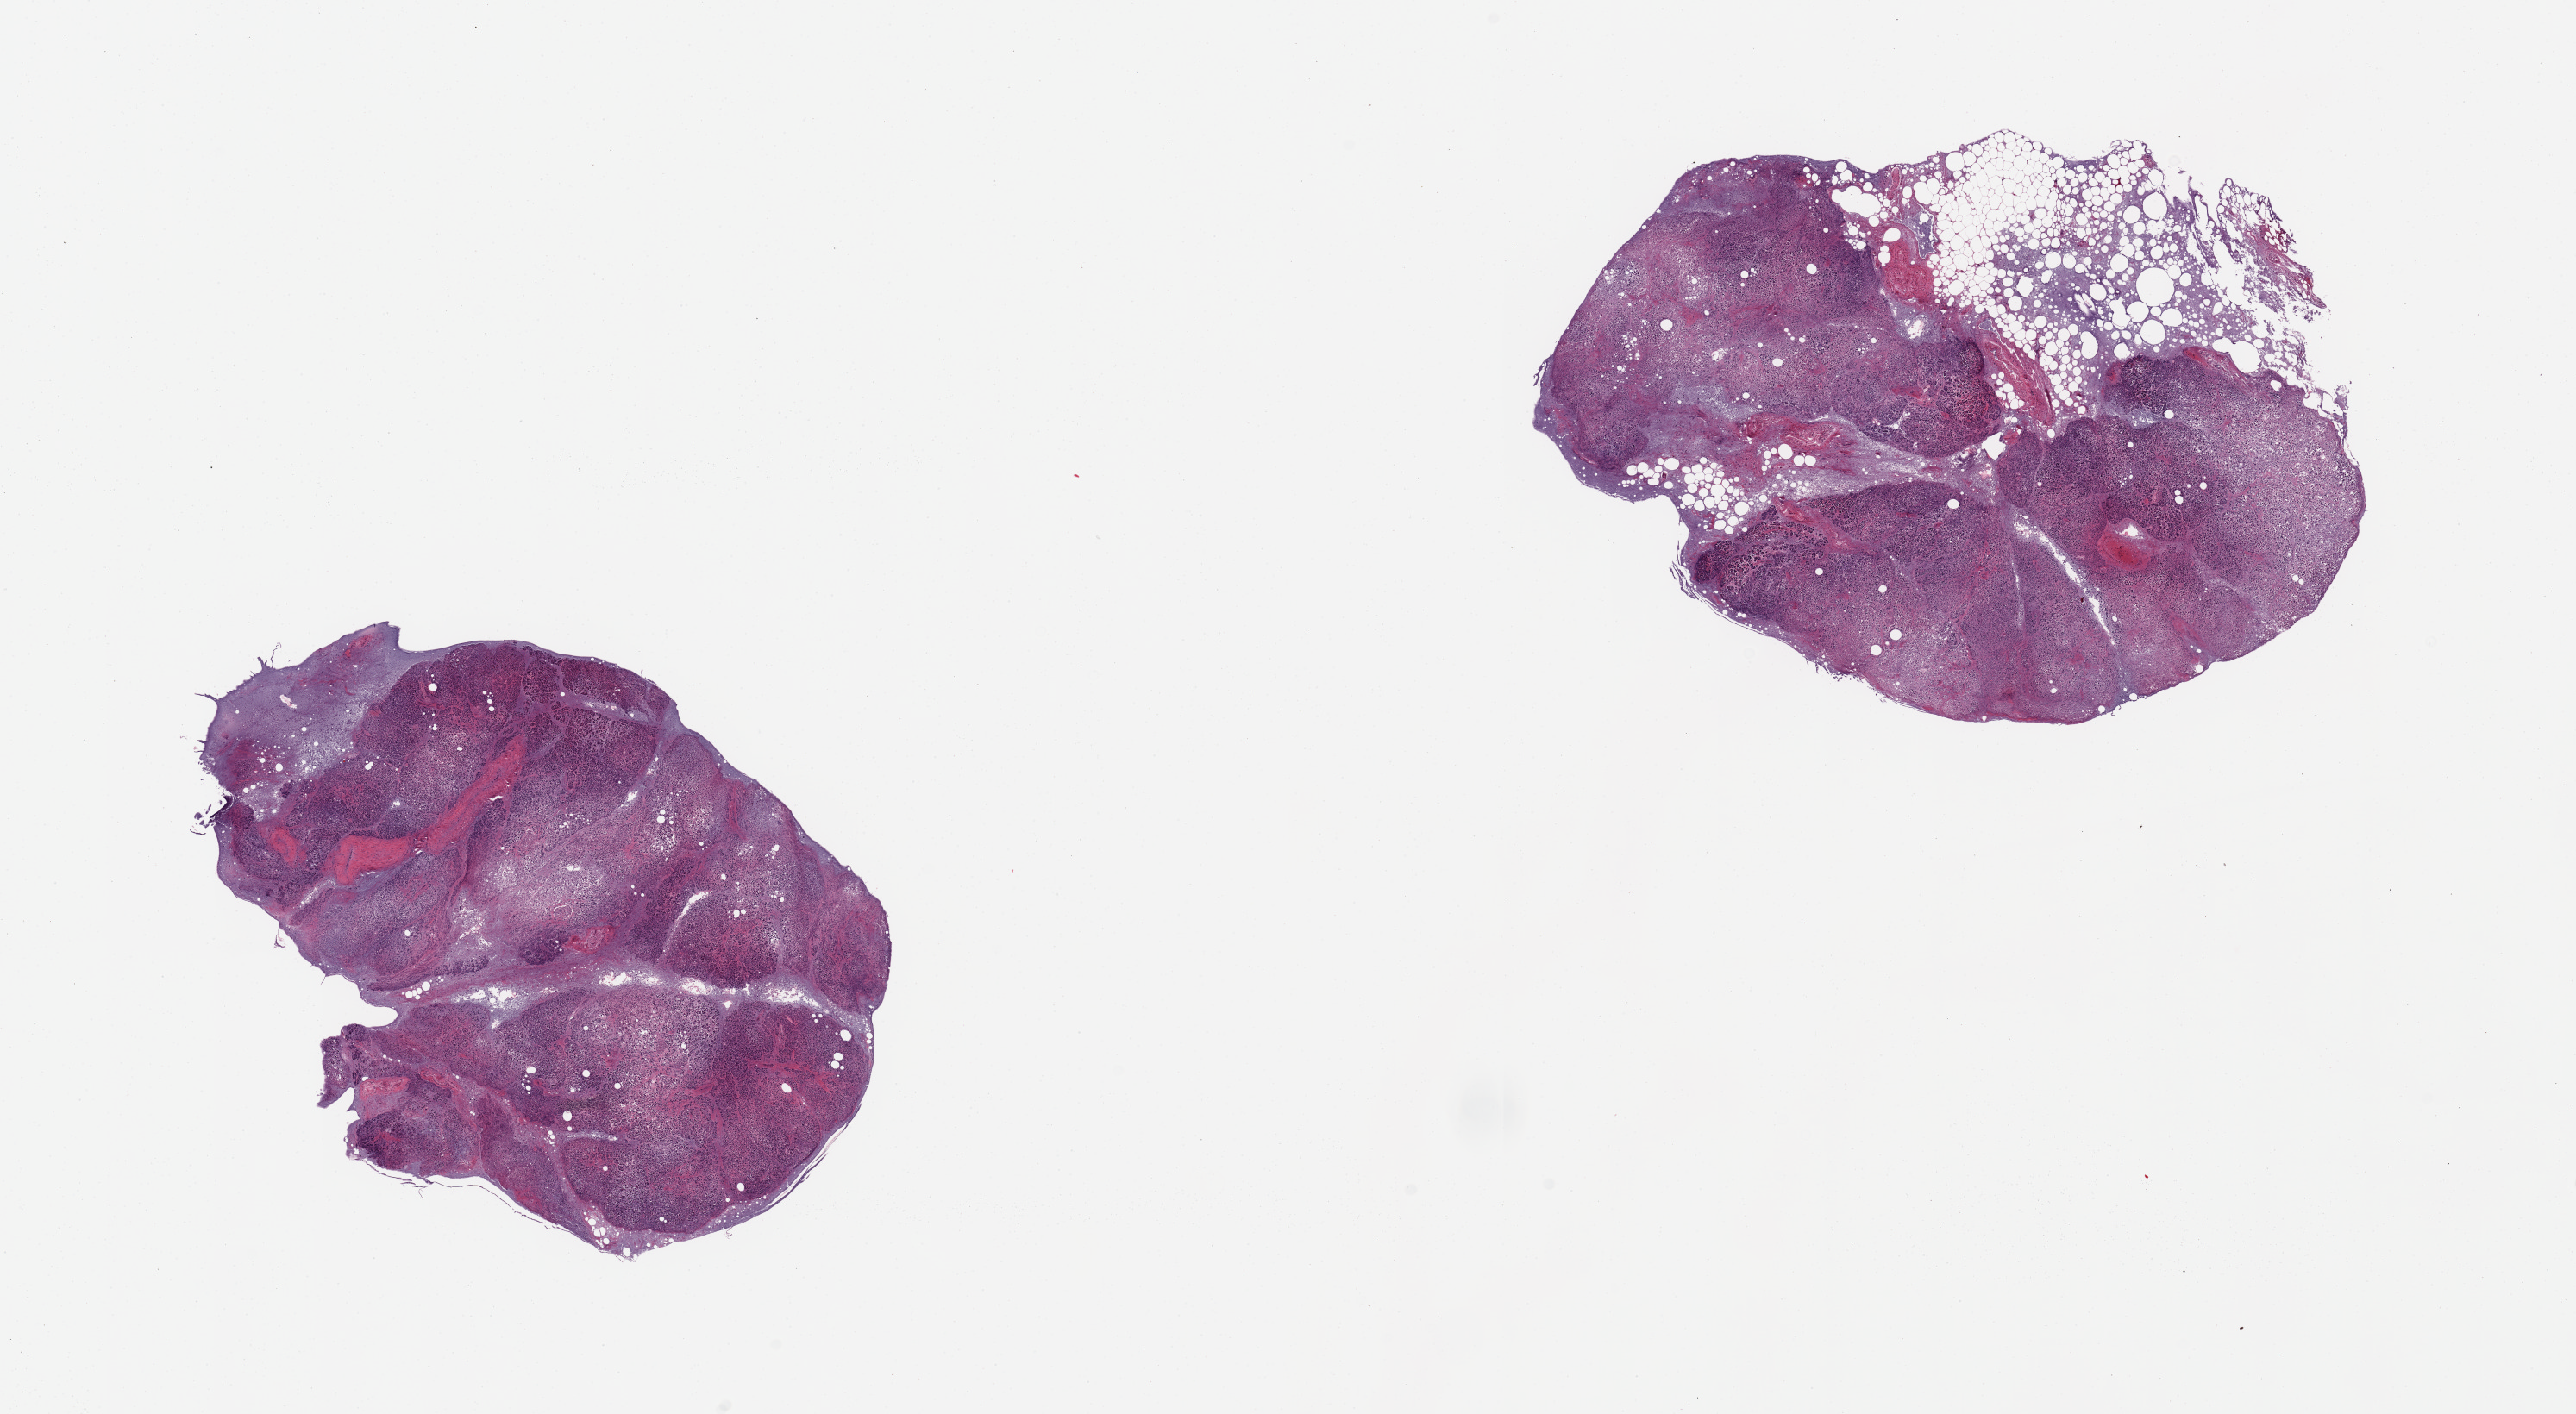
Whole-slide image, hematoxylin and eosin (H&E) stain, brightfield — whole scanned area (about 23.6 x 13.0 mm) shown as a low-resolution overview, PAXgene-fixed, paraffin-embedded tissue, target tissue: pancreas, donor tissue sample. Donor sex: female.
Pathologist's review note for this sample: 2 pieces, severe saponification/autolysis.